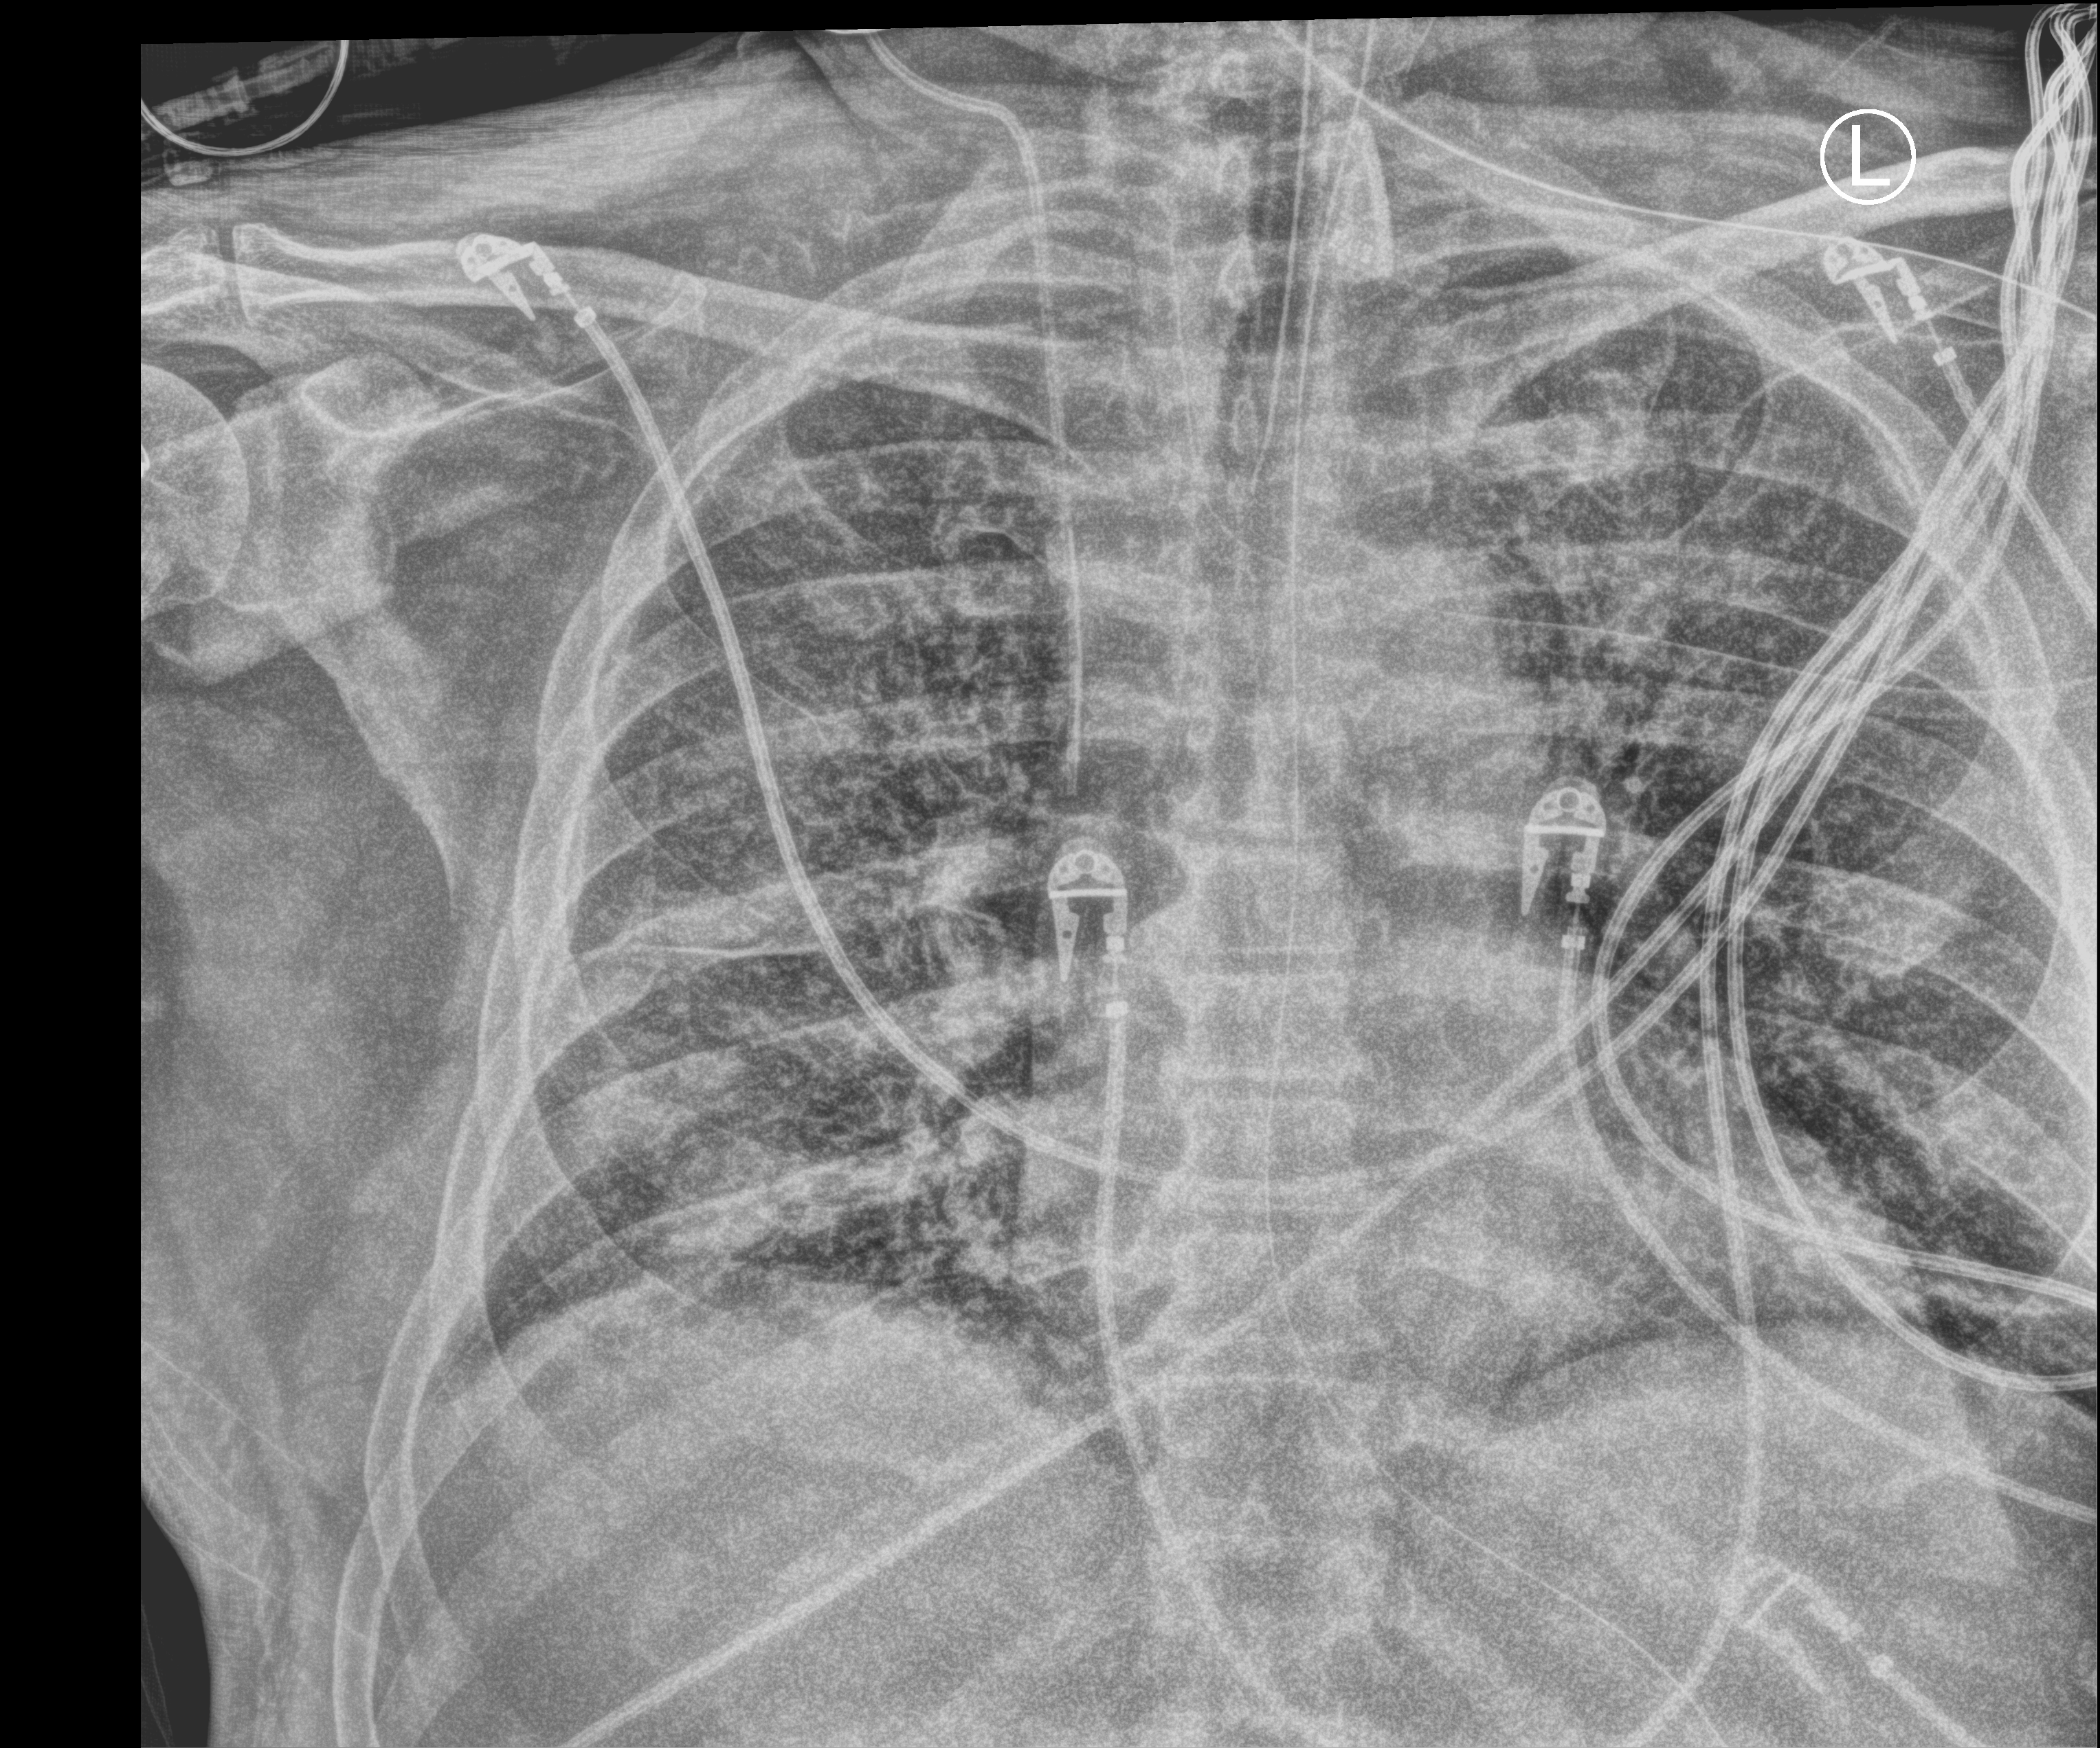
Portable chest radiograph, anteroposterior (AP) projection. Patient hospitalised with COVID-19; male, aged 60–74 years.
Admission-level facts for this patient (not findings on this image; timing relative to this image not recorded): admitted to intensive care during this hospital stay: yes; chronic kidney disease (admission record): no; mechanically ventilated during this hospital stay: yes.